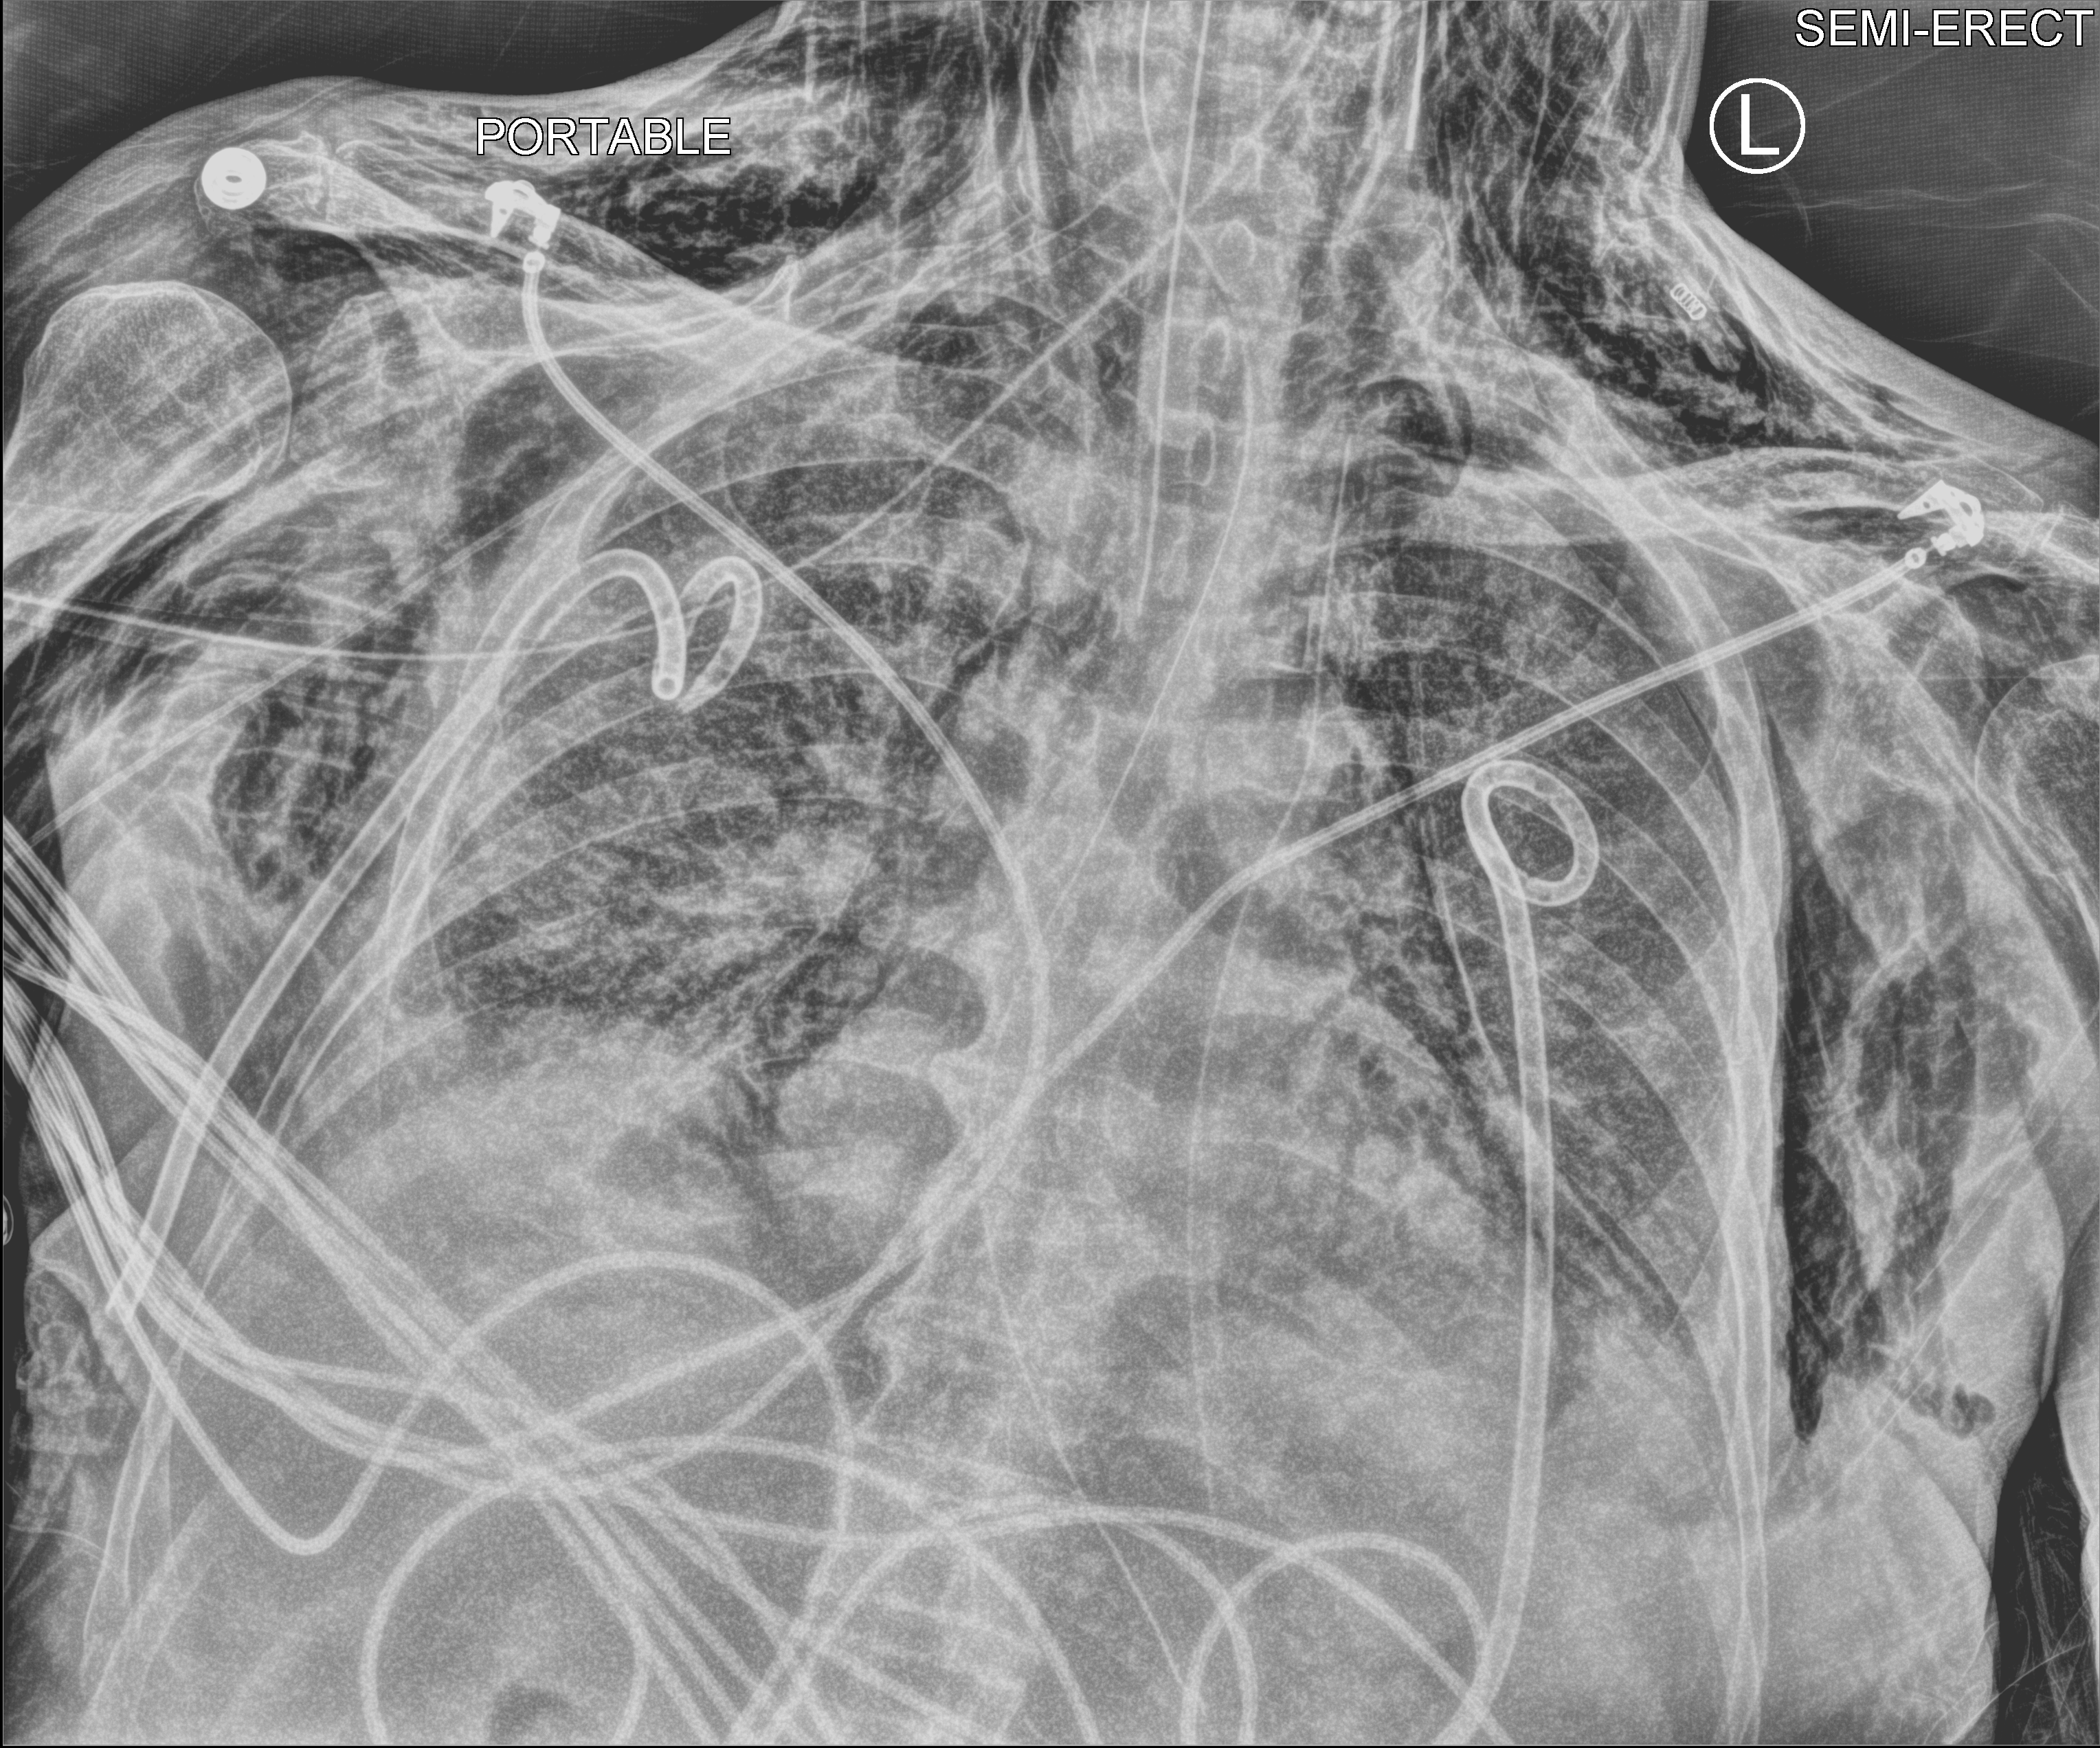
Portable chest radiograph; anteroposterior (AP) projection. Patient hospitalised with COVID-19; male, aged 75–90 years.
Hospital-stay facts (about this admission, not read from this image; timing relative to this image not recorded): COPD (admission record): no; smoking status (admission record): never.